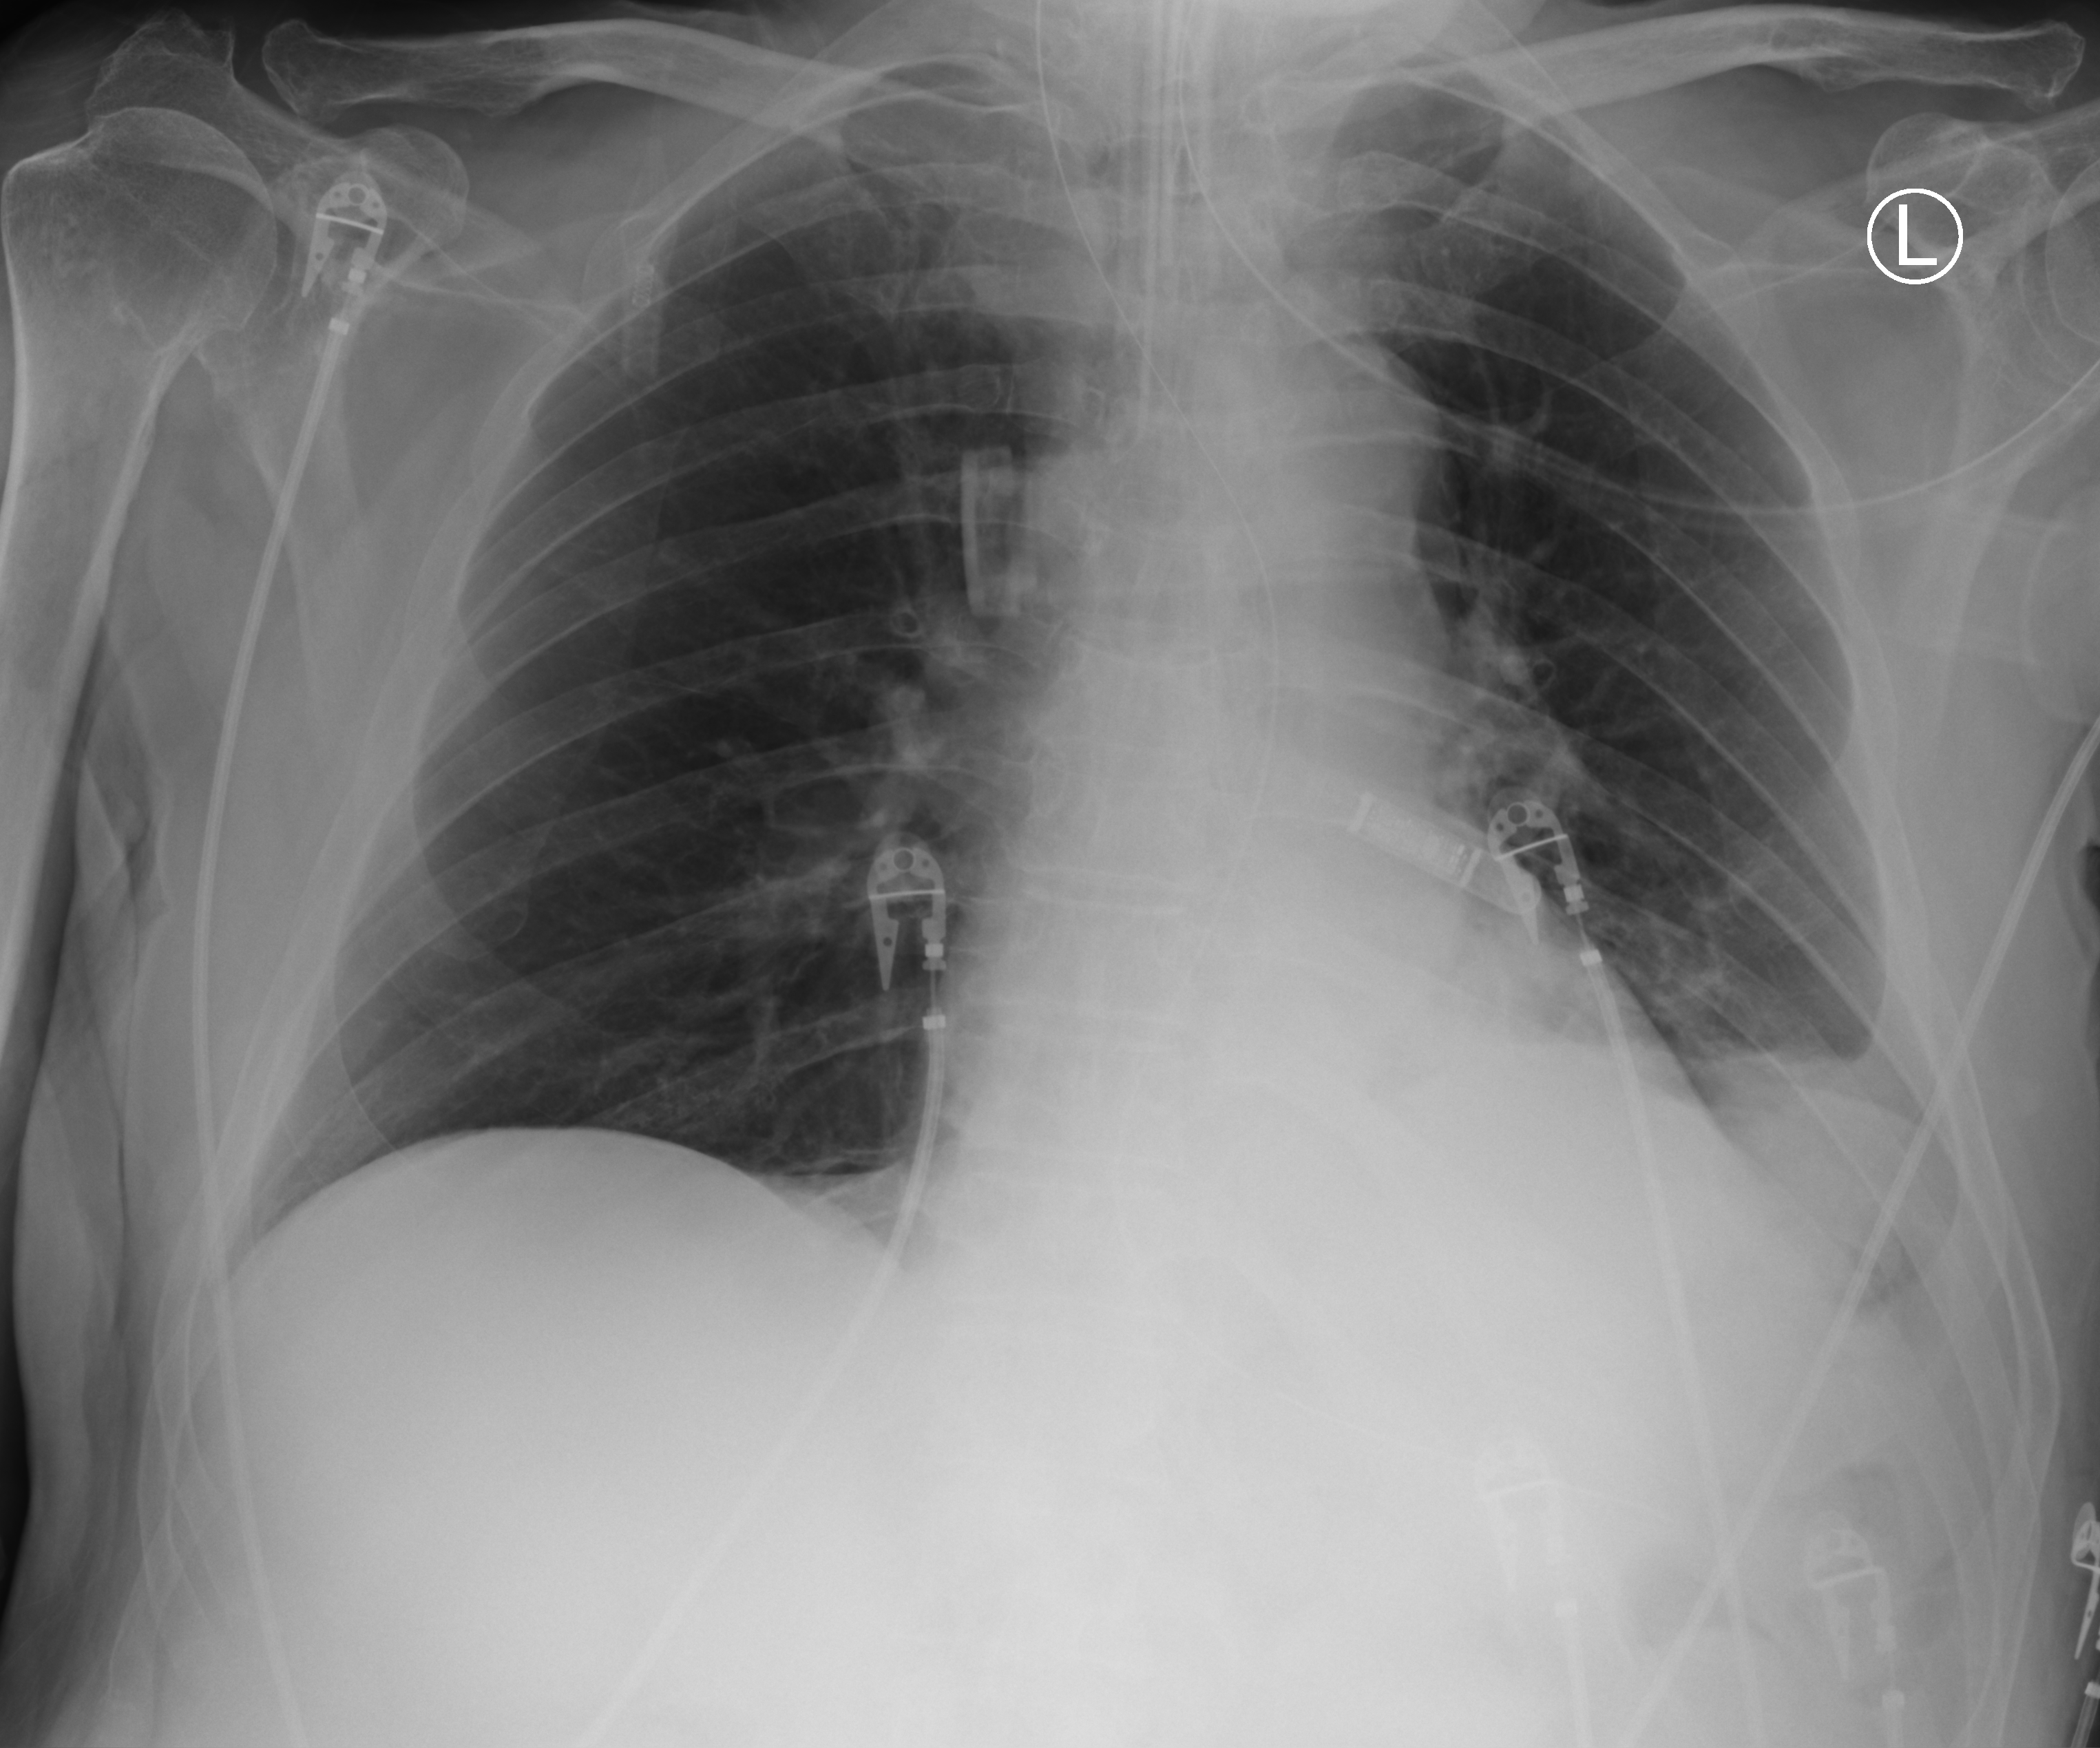
Bedside chest radiograph (computed radiography); anteroposterior (AP) projection. Male patient hospitalised with COVID-19, age 75–90 years.
Admission-level facts for this patient (not findings on this image; timing relative to this image not recorded):
- admitted to intensive care during this hospital stay: yes
- mechanically ventilated during this hospital stay: no